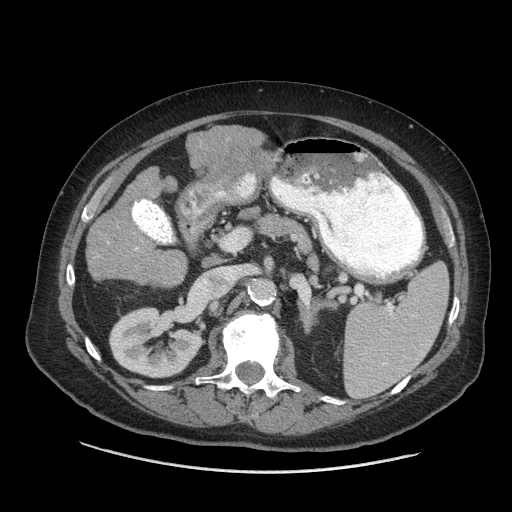
Contrast-enhanced abdominal CT (liver protocol), one axial slice. Reconstruction kernel STANDARD. 140 kVp. Soft-tissue window (W 400 / L 40 HU). 512 × 512 image matrix. Case-level facts recorded for this patient, not image findings: diagnosis: hepatocellular carcinoma (patient treated with transarterial chemoembolisation; whether this scan precedes or follows treatment is not stated here); TNM stage (as recorded): Stage-I; Child-Pugh class: A; tumour differentiation: well differentiated.
Structures marked on this image (semi-automatically segmented with operator editing):
- liver parenchyma outside the tumour (the mass and vessels are separate outlines, so this box may not span the whole liver): box from (x=88, y=132) to (x=211, y=286) px
- liver vessels: (x=135, y=247)–(x=137, y=249)